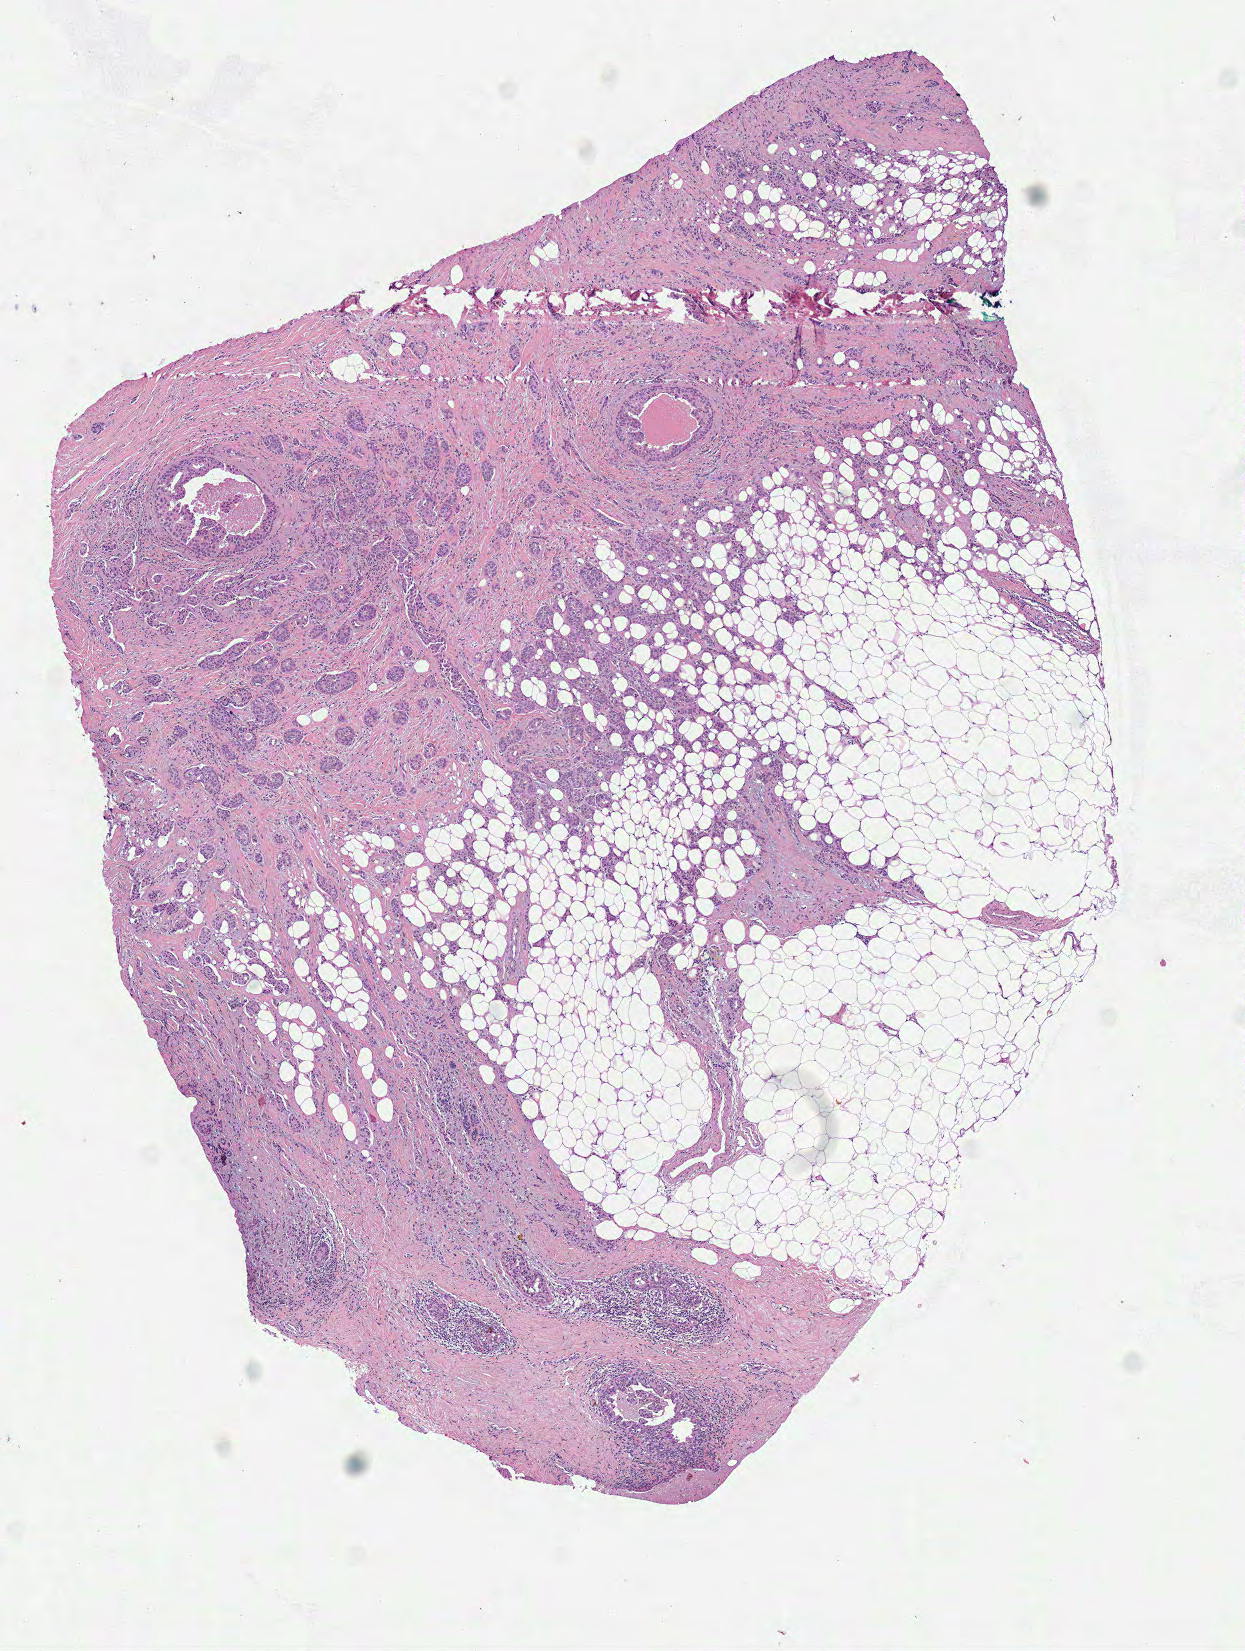
H&E-stained whole-slide image, low-resolution overview of the scanned area, about 4.9 x 6.5 mm (acquisition: 40x scan). Formalin-fixed paraffin-embedded (FFPE) diagnostic section. Primary tumour sample from the breast. Female, age 62 years at initial diagnosis.
Histologic diagnosis: Infiltrating duct carcinoma, NOS. AJCC pathologic stage: IIB (7th edition). Lymph nodes positive (case pathology): 1 of 1 examined.